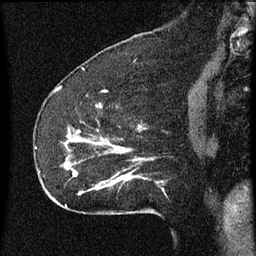
Breast MRI (dynamic contrast-enhanced), one sagittal slice. Position 20 of 60 along the scan axis. Dynamic contrast-enhanced series, image 2 of 3 at this slice position (ordered by acquisition). 1.5 T. TE 4.2 ms, TR 8 ms. 2 mm slice thickness. 256 × 256 image matrix. Female patient, age 52 years.
Outlined on this slice (semi-automatic segmentation, software-assisted and operator-edited):
- analysis volume of interest (the breast-tissue region the enhancement analysis was run in; not a lesion): box from (x=54, y=120) to (x=164, y=207) px
- tumour enhancement mask (voxels above the 70 % enhancement threshold inside the analysis volume of interest): (x=65, y=130)–(x=164, y=191)